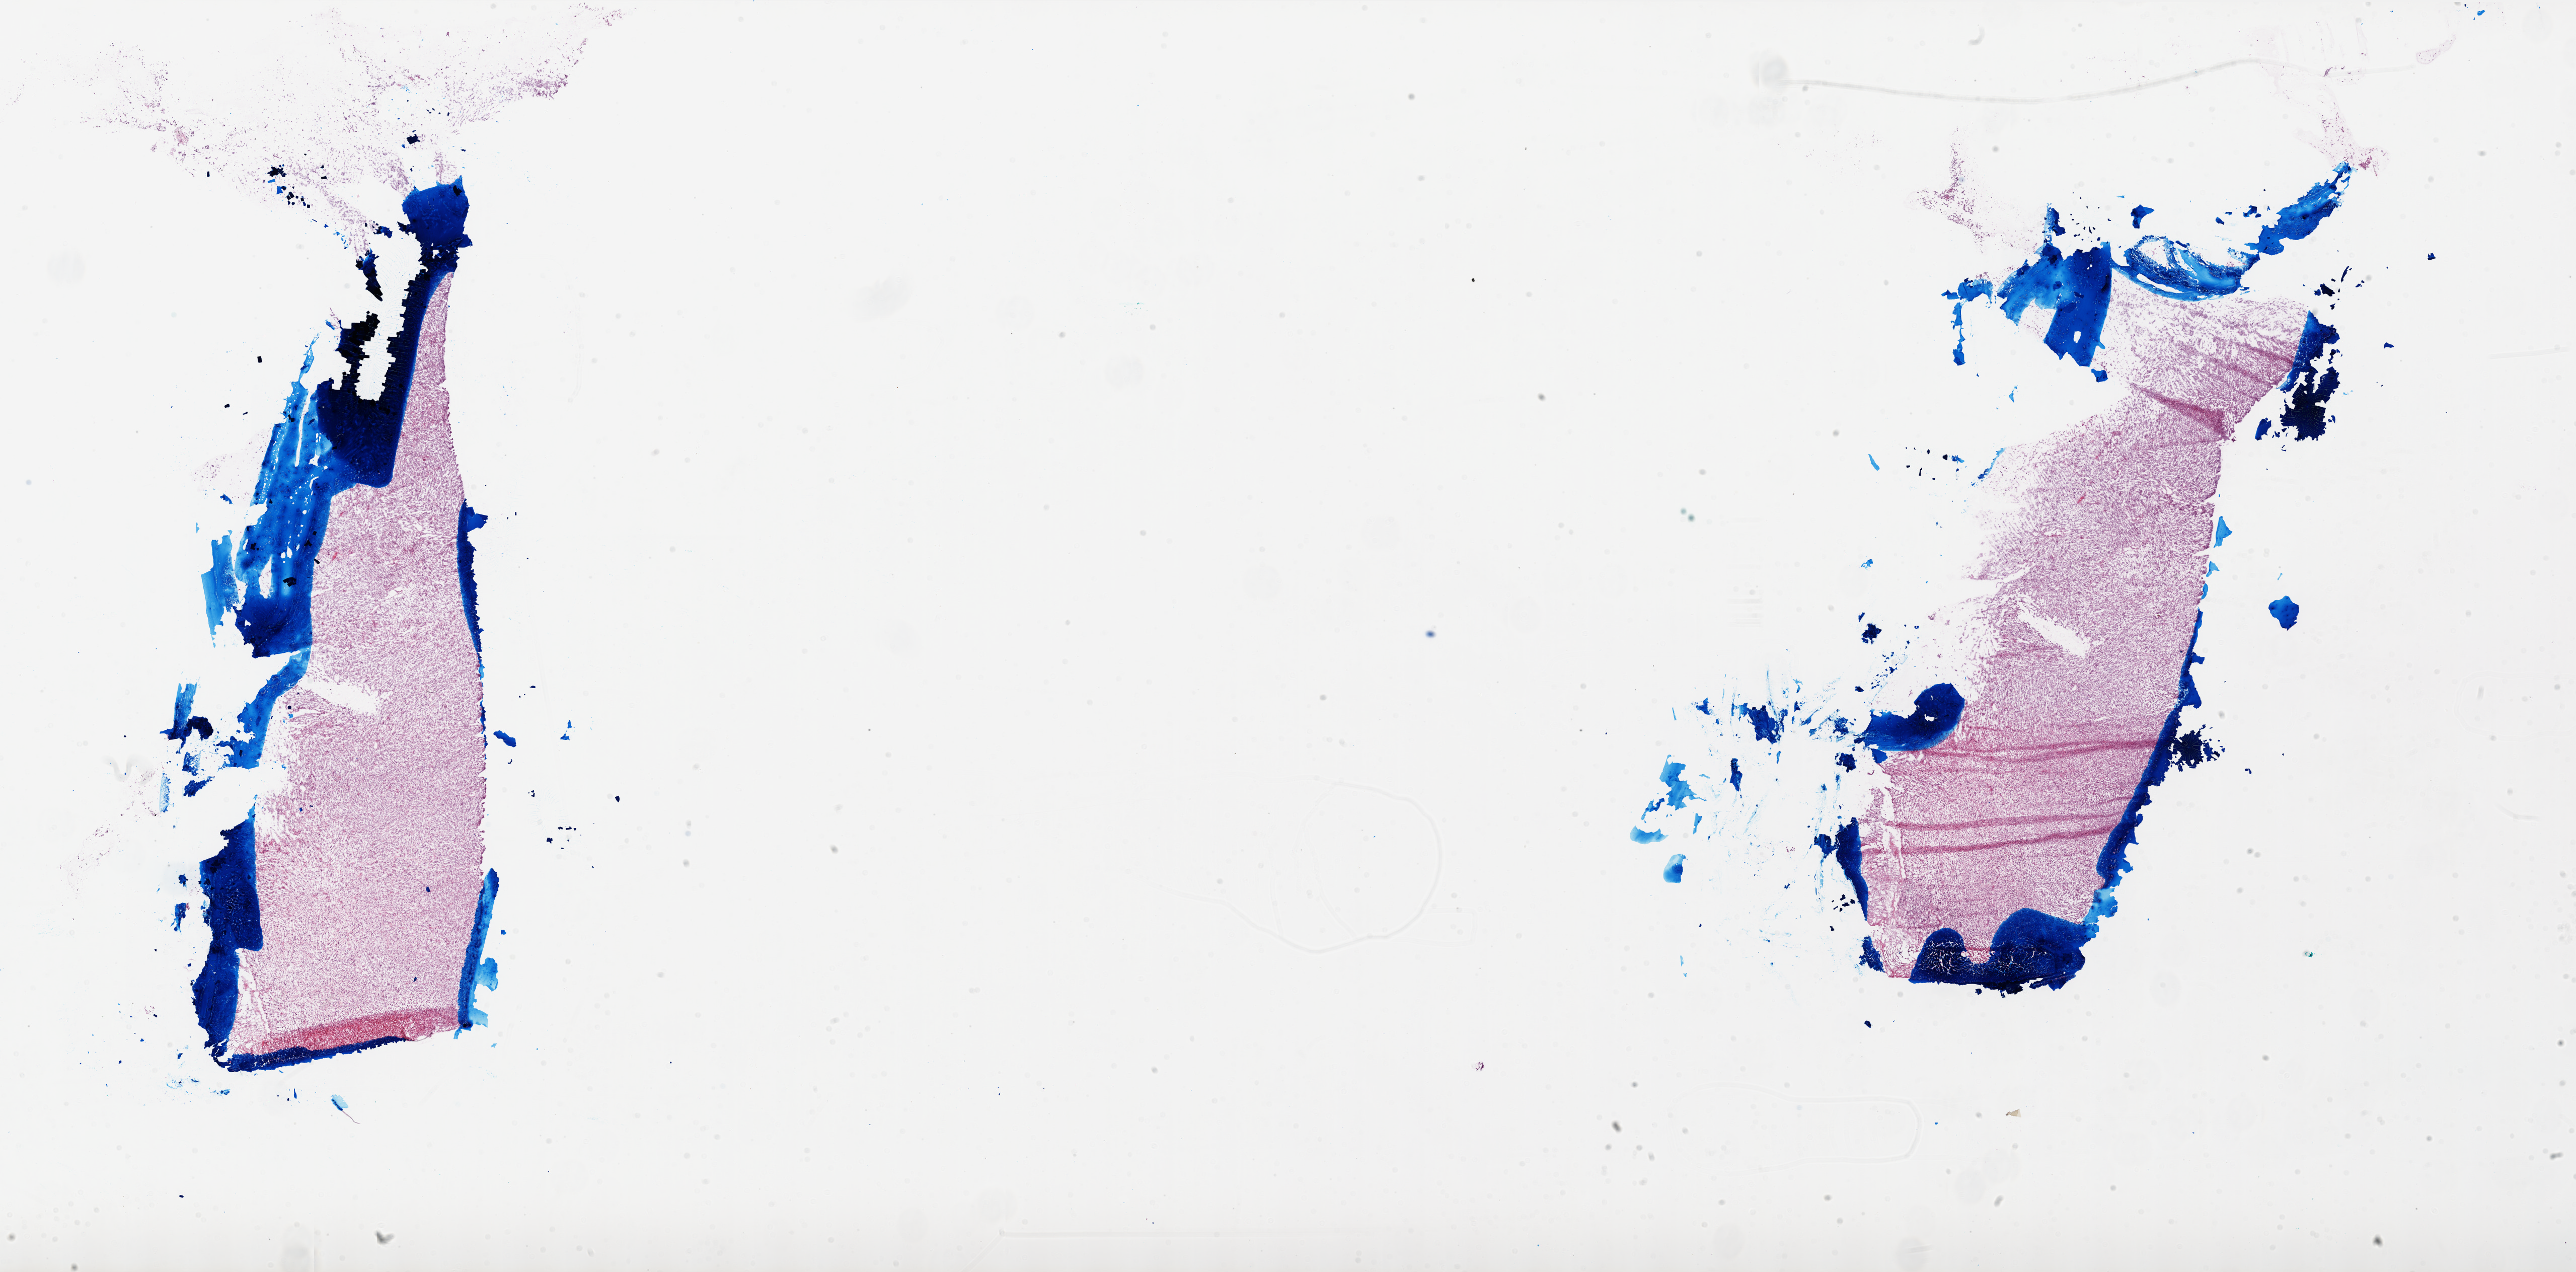
H&E whole-slide image — whole scanned area (about 41.0 x 20.2 mm, from a 20x scan) shown as a low-resolution overview, frozen section from the top of the tissue portion, primary tumour sample from the brain. Patient: female, age at initial diagnosis 20 years. Pathologist review of this section (percent, as recorded): tumour cells 100%, tumour nuclei 100%, normal cells 0%, stromal cells 0%, necrosis 0%.
* pathologic diagnosis: Glioblastoma